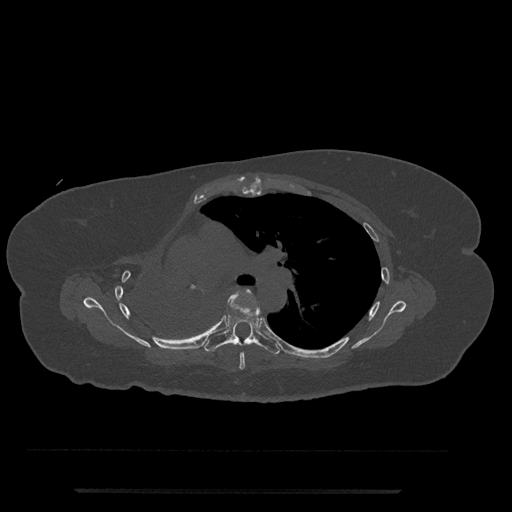
CT including the spine, one axial slice; position 510 of 797 along the scan axis; reconstruction kernel Br40s/3; bone window (W 1800 / L 400 HU); 0.5 mm slice thickness; 512 × 512 image matrix. Female patient, age 51 years. Case-level facts recorded for this patient, not image findings: primary cancer: neuro; vertebrae with lytic lesions (as recorded): T8.
Structures marked on this image (semi-automatically segmented with operator editing):
- T5 vertebra: bounding box (x1, y1, x2, y2) in pixels: (239, 289, 265, 370)
- T6 vertebra: (204, 299, 281, 355)